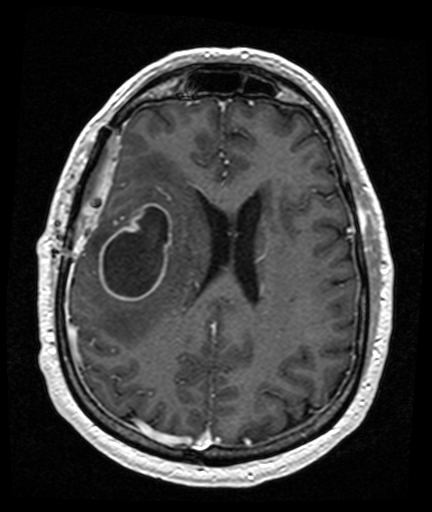
Brain MRI from a brain-tumour surgery series, one axial slice; slice 62 of 176 in the series (ordered by position); T1-weighted post-contrast; 1 mm slice thickness; 432 × 512 image matrix, field of view 194 × 230 mm. Case-level facts recorded for this patient, not image findings: histopathology: Glioblastoma; WHO grade: 4.
Outlined on this slice (manually delineated by an expert):
- tumour: box from (x=100, y=203) to (x=173, y=301) px